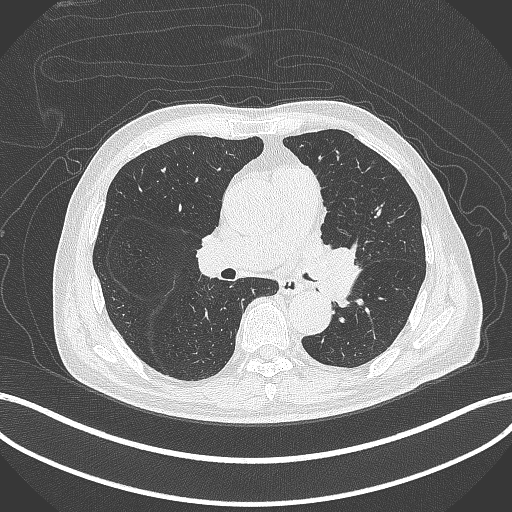
Chest CT, one axial slice. Position 237 of 417 along the scan axis. 120 kVp. Lung window (W 1500 / L -600 HU). 512 × 512 image matrix, field of view 400 × 400 mm. Patient: male, 77 years. From the clinical record (not read from this slice): clinical TNM (as recorded): T3 N1 M0.
Annotated regions visible in this slice (rectangle marked by the reading radiologist):
- lung tumour (recorded histology: adenocarcinoma): bounding box (x1, y1, x2, y2) in pixels: (308, 240, 363, 306)